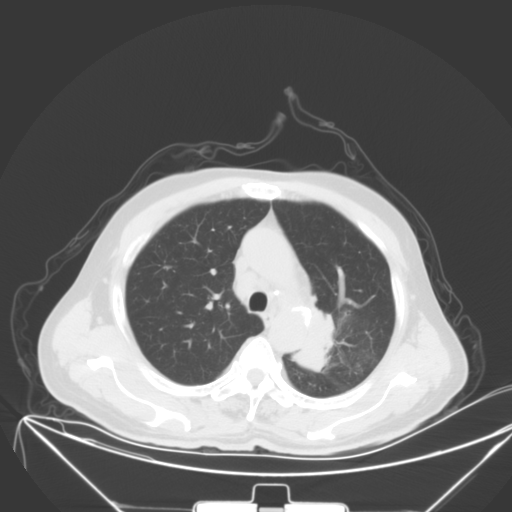
Chest CT, one axial slice; position 43 of 64 along the scan axis; 120 kVp; lung window (W 1500 / L -600 HU); 5 mm slice thickness; 512 × 512 image matrix. Patient: male, 58 years. From the clinical record (not read from this slice): clinical TNM (as recorded): T2b N3 M1b.
Annotated regions visible in this slice (rectangle marked by the reading radiologist):
- lung tumour (recorded histology: adenocarcinoma): bounding box <304,304,337,372> (left, top, right, bottom; pixels)